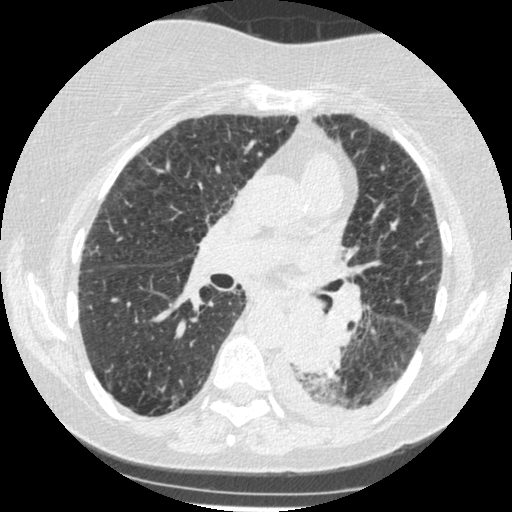
Chest CT (low-dose screening protocol), one axial image, third annual screen, lung window (W 1500 / L -600 HU), 1.25 mm slice thickness. Female participant, aged 60 years at enrolment. Former smoker at enrolment.
Expert reader's lesion annotation, bounding box [x1, y1, x2, y2] px = [271, 306, 342, 374]. Screening reader's record for this exam (one nodule recorded; not confirmed to be the boxed lesion): non-calcified nodule or mass ≥4 mm, left lower lobe, 54 × 38 mm, smooth margins, soft tissue attenuation, pre-existing on the prior screen: yes; interval growth: yes. Official screen result: positive, other. Participant outcome: lung cancer diagnosed 15 days after this screen — small cell carcinoma, NOS, left lower lobe, undifferentiated (G4), stage IV (AJCC 6th edition), 69 mm at pathology.